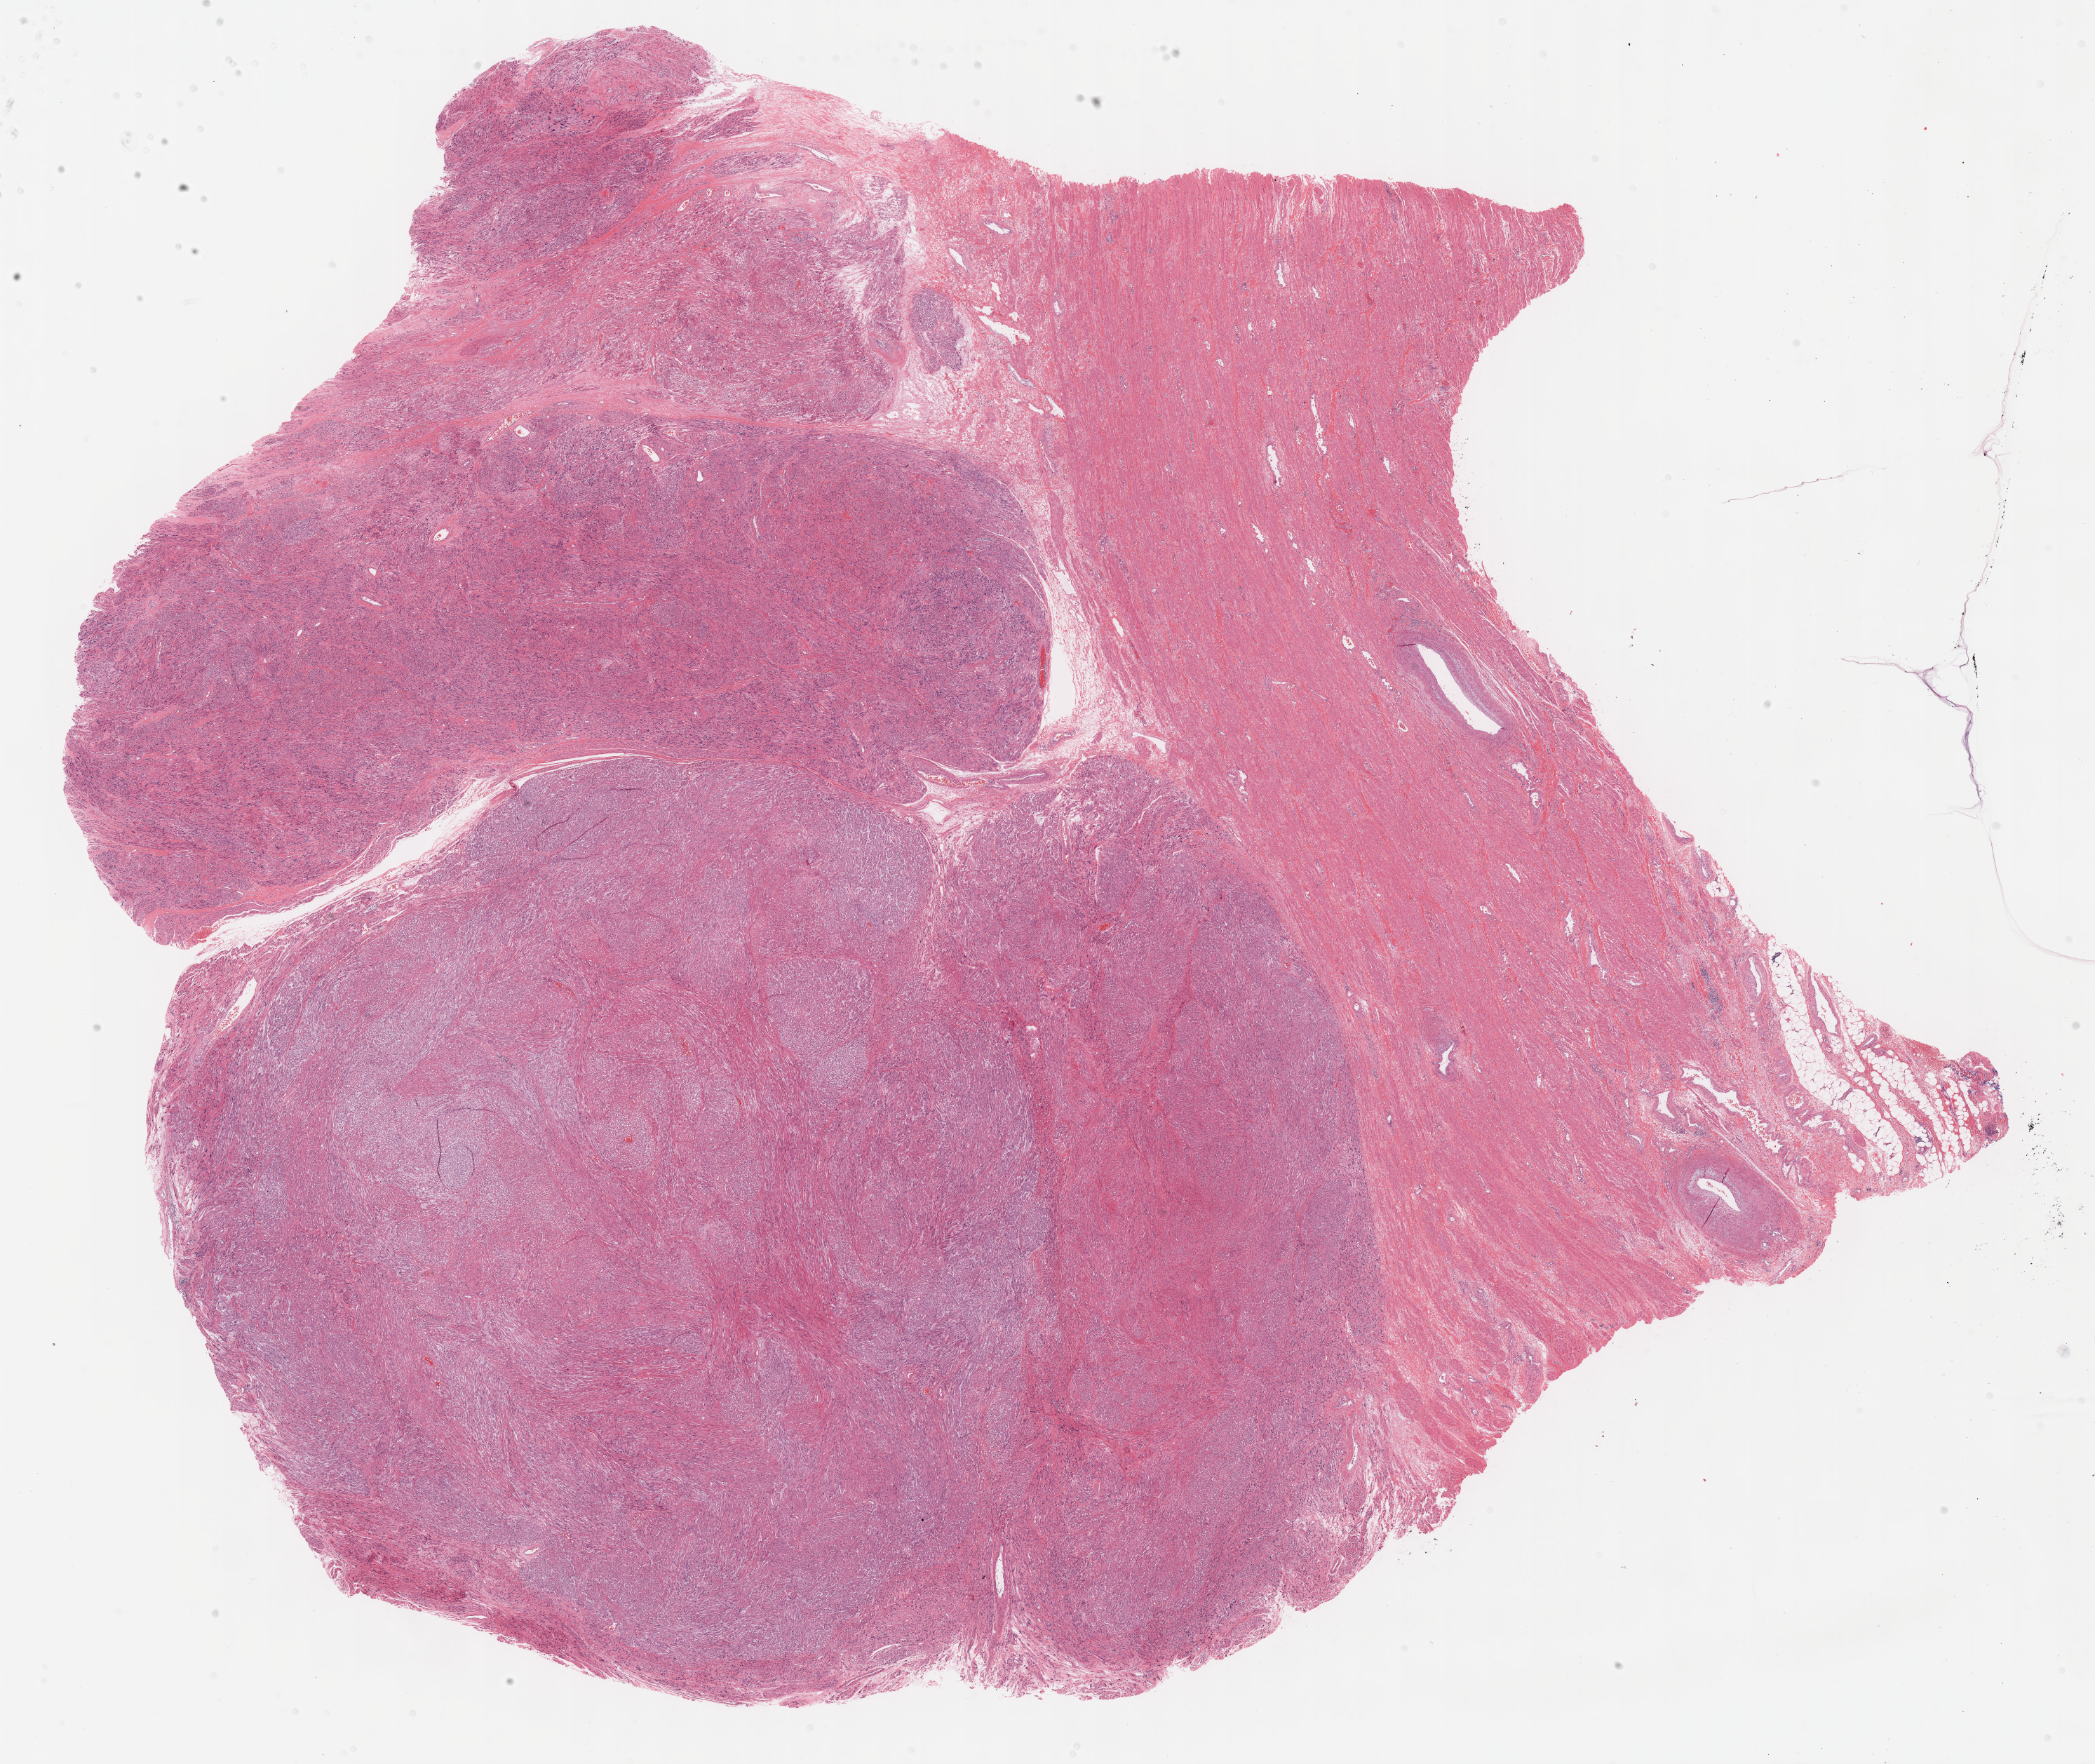
Whole-slide histology image, H&E — shown as a low-resolution overview of the whole scanned area (about 24.2 x 20.3 mm). Formalin-fixed paraffin-embedded (FFPE) diagnostic section. Retroperitoneum and peritoneum, primary tumour sample. Patient: male, age at initial diagnosis 44 years.
Histologic diagnosis: Leiomyosarcoma, NOS (retroperitoneum).